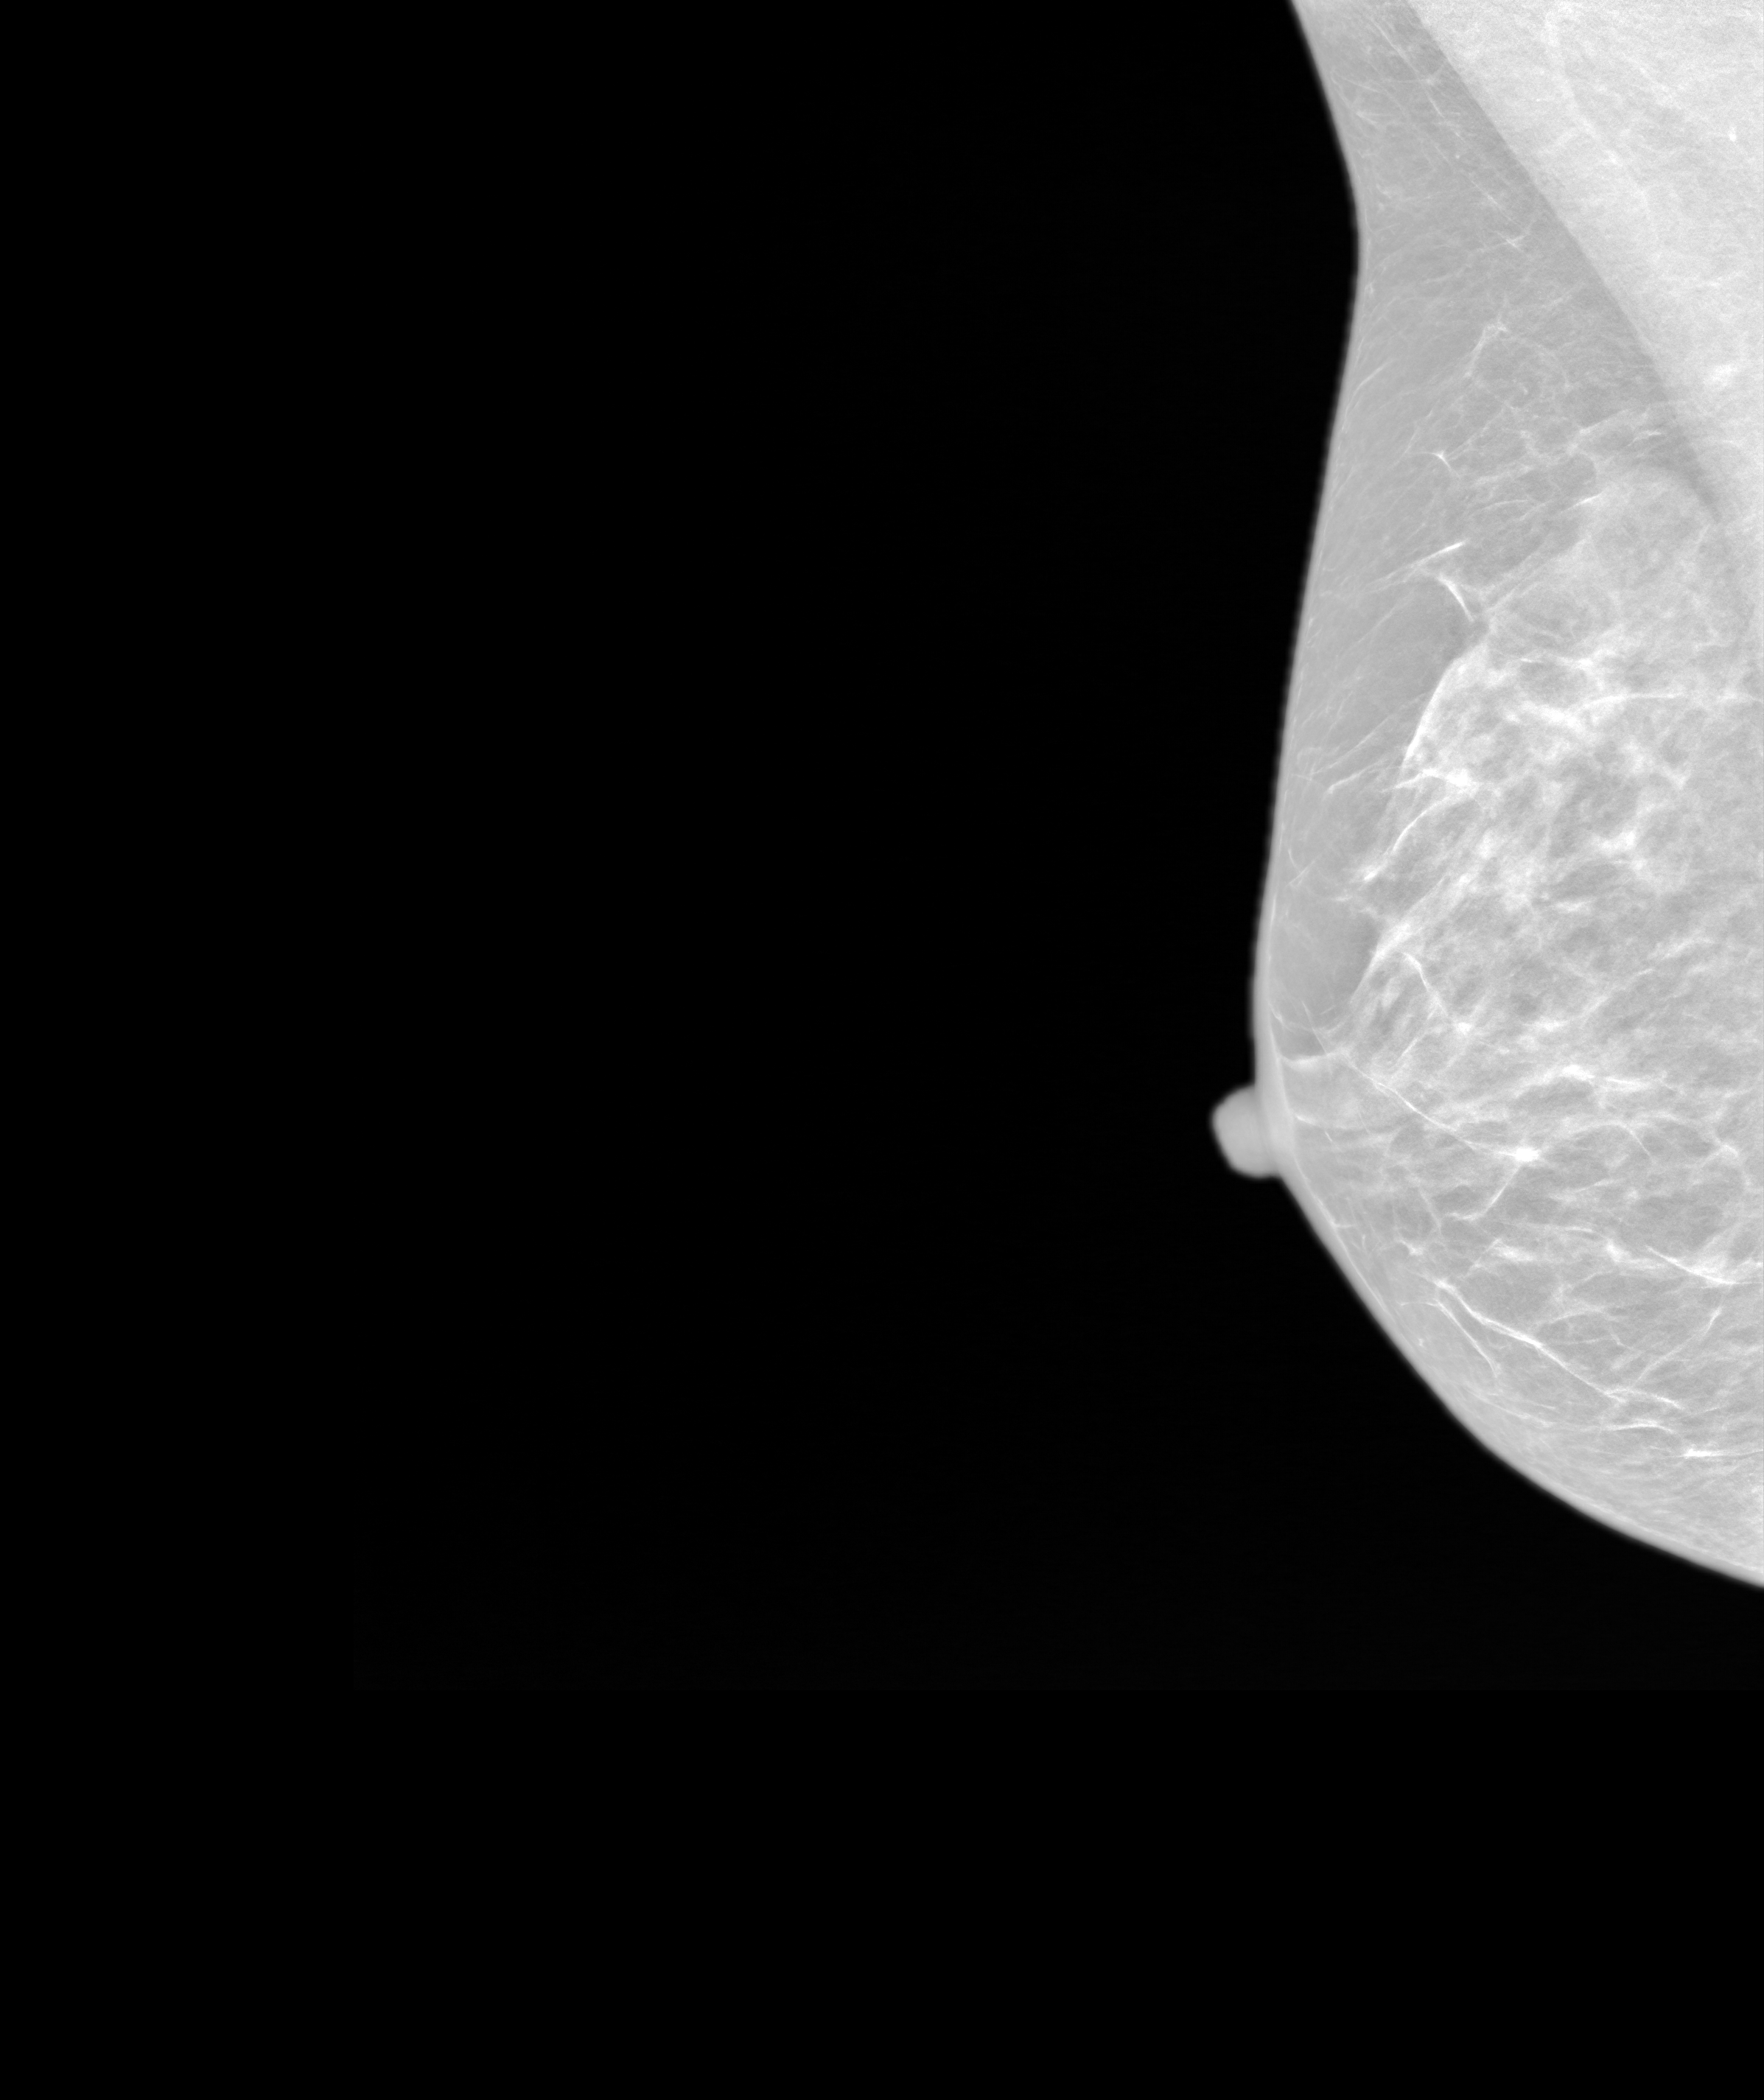
Screening examination. Patient: female, 62 years.
Image type: synthesized 2-D view from tomosynthesis. Breast: right. Projection: MLO view.